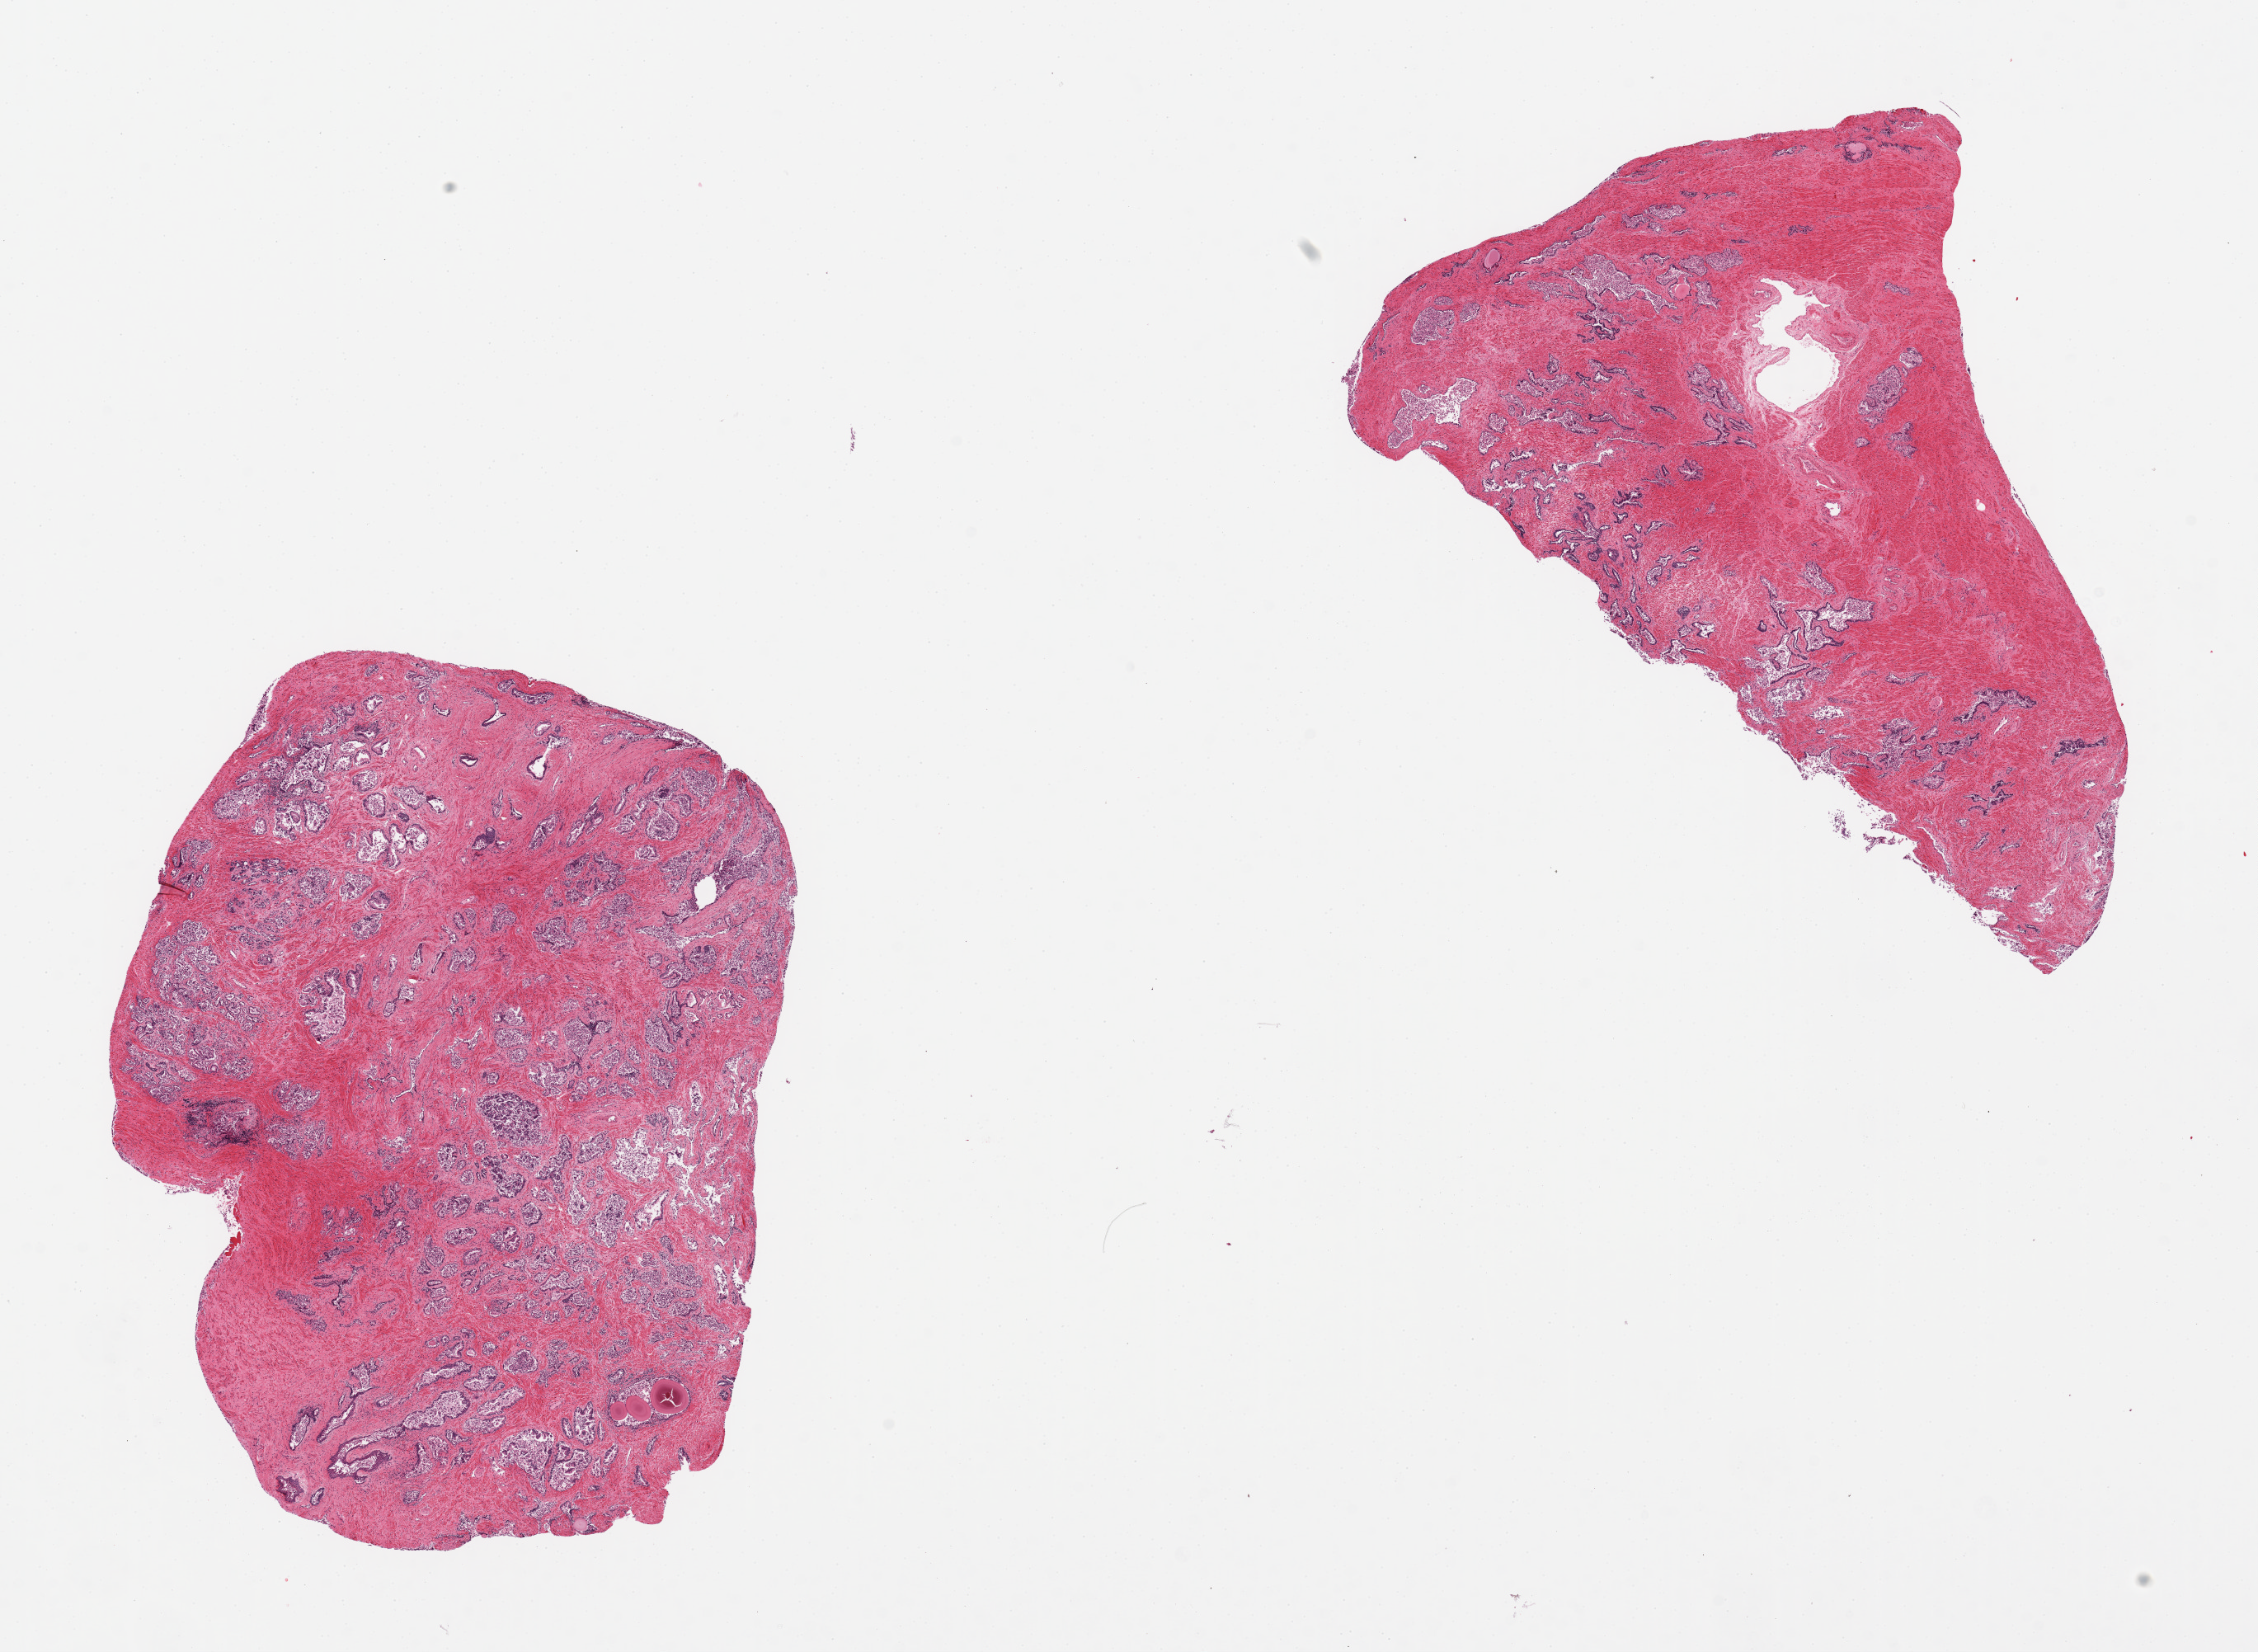
Digitized haematoxylin and eosin-stained section, shown as a low-resolution overview of the whole scanned area (about 21.7 x 15.8 mm), PAXgene-fixed paraffin-embedded (PFPE) section, target tissue: prostate, donor tissue sample. Donor sex: male.
Pathologist's review note for this sample: 2 pieces, glands largely sloughed, focal chronic inflammation.